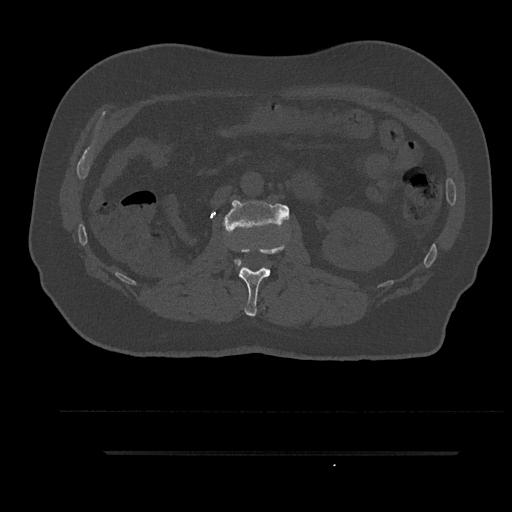
CT including the spine, one axial slice. Position 147 of 797 along the scan axis. Reconstruction kernel Br40s/3. Bone window (W 1800 / L 400 HU). 512 × 512 image matrix, field of view 432 × 432 mm. Male patient, age 63 years. From the clinical record (not read from this slice): primary cancer: renal.
Structures marked on this image (semi-automatically segmented with operator editing):
- L1 vertebra: bounding box <239,244,285,316> (left, top, right, bottom; pixels)
- L2 vertebra: <222,200,290,266>